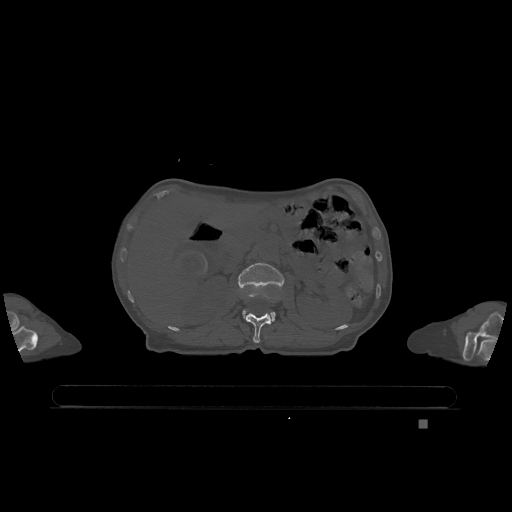
CT including the spine, one axial slice. Position 451 of 1317 along the scan axis. Bone window (W 1800 / L 400 HU). 0.5 mm slice thickness. 512 × 512 image matrix. Female patient, age 74 years. Case-level facts recorded for this patient, not image findings: primary cancer: lung.
Outlined on this slice (semi-automatic segmentation, software-assisted and operator-edited):
- L1 vertebra: bounding box (x1, y1, x2, y2) in pixels: (245, 313, 271, 343)
- L2 vertebra: (238, 263, 284, 322)